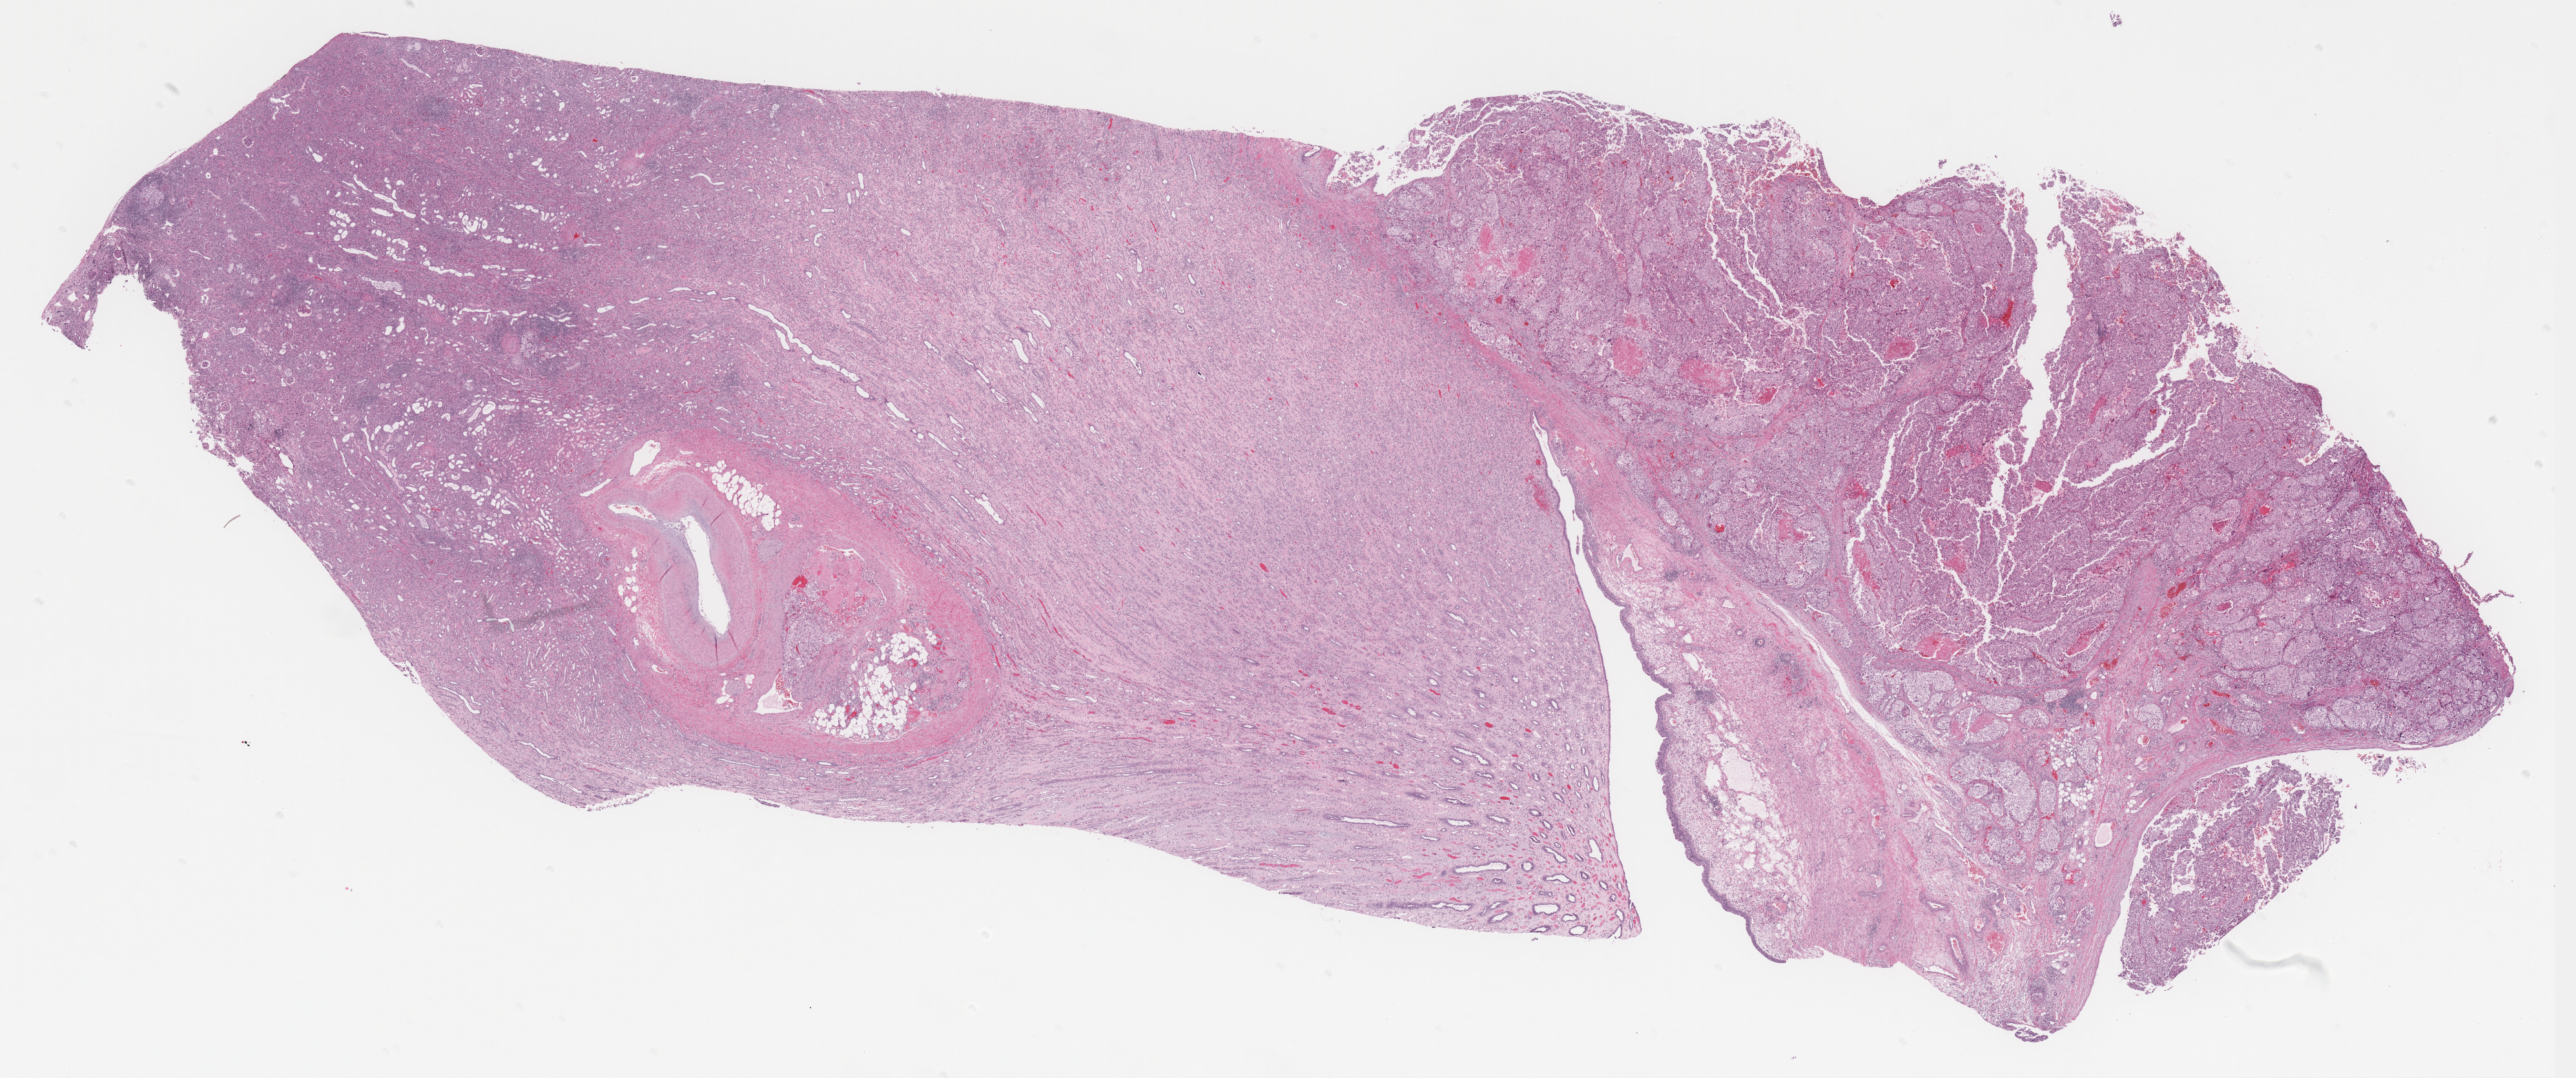
H&E whole-slide image, shown as a low-resolution overview of the whole scanned area (about 31.9 x 13.4 mm, acquisition: 40x scan), FFPE section, sample: primary tumour, kidney. Female, age 51 years at initial diagnosis.
* diagnosis: Renal cell carcinoma, chromophobe type
* AJCC pathologic stage: IV (6th edition)